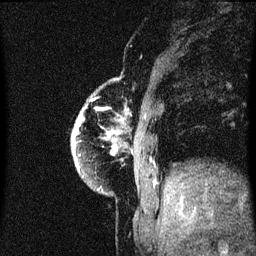
Breast MRI (dynamic contrast-enhanced), one sagittal slice. Slice 9 of 60 in the series (ordered by position). Dynamic contrast-enhanced series, image 2 of 3 at this slice position (ordered by acquisition). 1.5 T. TE 4.2 ms, TR 8.4 ms. 2 mm slice thickness. 256 × 256 image matrix. Female patient, age 60 years.
Outlined on this slice (semi-automatically segmented with operator editing):
- analysis volume of interest (the breast-tissue region the enhancement analysis was run in; not a lesion): box from (x=72, y=88) to (x=115, y=193) px
- tumour enhancement mask (voxels above the 70 % enhancement threshold inside the analysis volume of interest): (x=72, y=118)–(x=113, y=167)